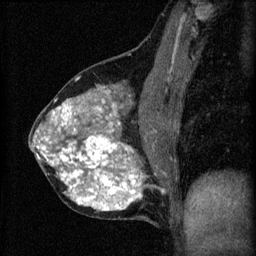
Breast MRI (dynamic contrast-enhanced), one sagittal slice; position 30 of 60 along the scan axis; 3 images stored at this slice position (order not interpretable as contrast timing); 1.5 T; TE 4.2 ms, TR 8.2 ms; 2 mm slice thickness; 256 × 256 image matrix, field of view 180 × 180 mm. Female patient, age 40 years.
Annotated regions visible in this slice (semi-automatically segmented with operator editing):
- analysis volume of interest (the breast-tissue region the enhancement analysis was run in; not a lesion): bounding box [x1, y1, x2, y2] px = [30, 76, 177, 219]
- tumour enhancement mask (voxels above the 70 % enhancement threshold inside the analysis volume of interest): [36, 96, 143, 211]